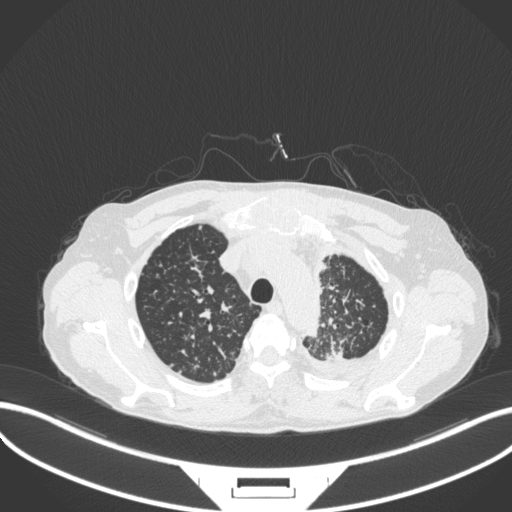
Chest CT, one axial slice. Slice 282 of 319 in the series (ordered by position). Reconstruction kernel B31f. 120 kVp. Lung window (W 1500 / L -600 HU). 1 mm slice thickness. 512 × 512 image matrix. Patient: male, 58 years. Case-level facts recorded for this patient, not image findings: clinical TNM (as recorded): T1c N3 M1.
Annotated regions visible in this slice (rectangle marked by the reading radiologist):
- lung tumour (recorded histology: adenocarcinoma): box from (x=323, y=346) to (x=344, y=364) px